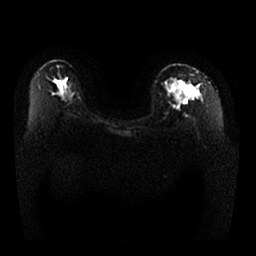
Breast MRI, one axial slice; diffusion-weighted series; image 2 of 4 stored at this slice position (different b-values; order by instance number); 1.5 T; 256 × 256 image matrix, field of view 350 × 350 mm. Female patient.
Outlined on this slice (outlined manually by an expert reader):
- tumour on diffusion-weighted imaging: bounding box [x1, y1, x2, y2] px = [183, 87, 194, 97]